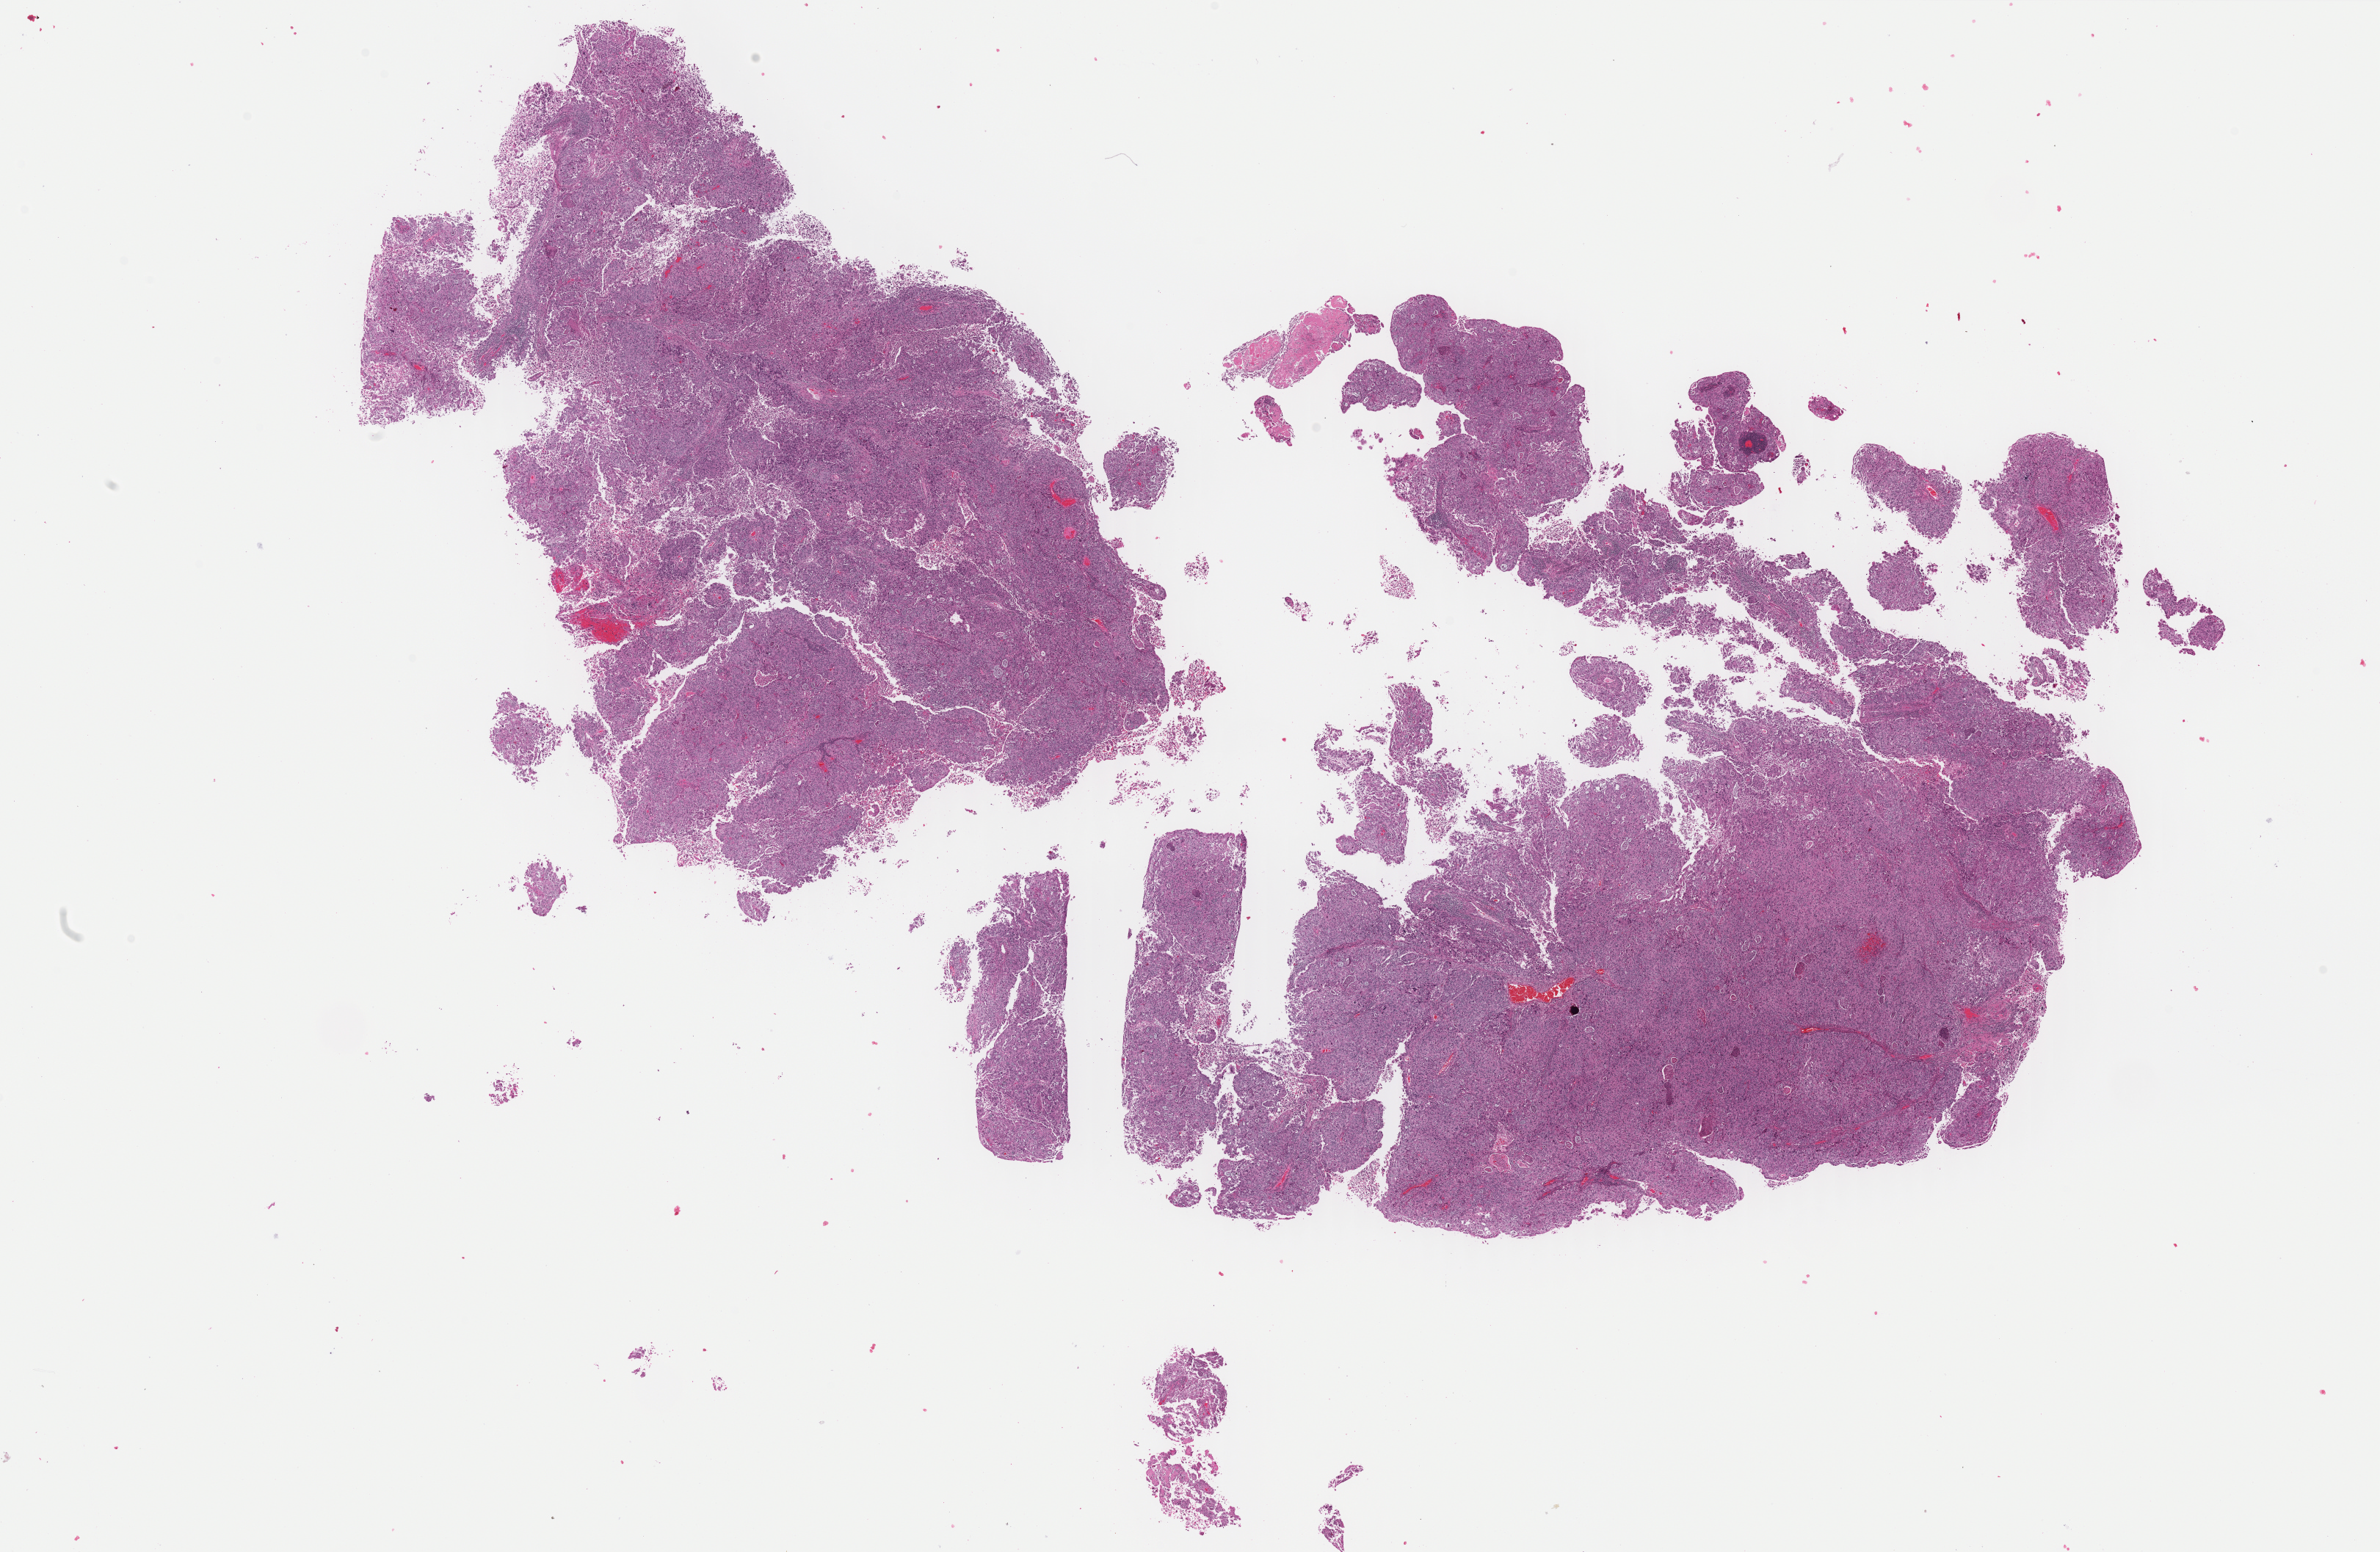
Hematoxylin and eosin (H&E) stained whole-slide image — low-resolution overview of the scanned area, about 25.7 x 16.7 mm; formalin-fixed paraffin-embedded (FFPE) diagnostic section; uterus, primary tumour sample. Female patient; age at initial diagnosis 66 years. Histologic grade: G3 (poorly differentiated).
Histologic diagnosis: Endometrioid adenocarcinoma, NOS (endometrium). FIGO stage: IIIC1.